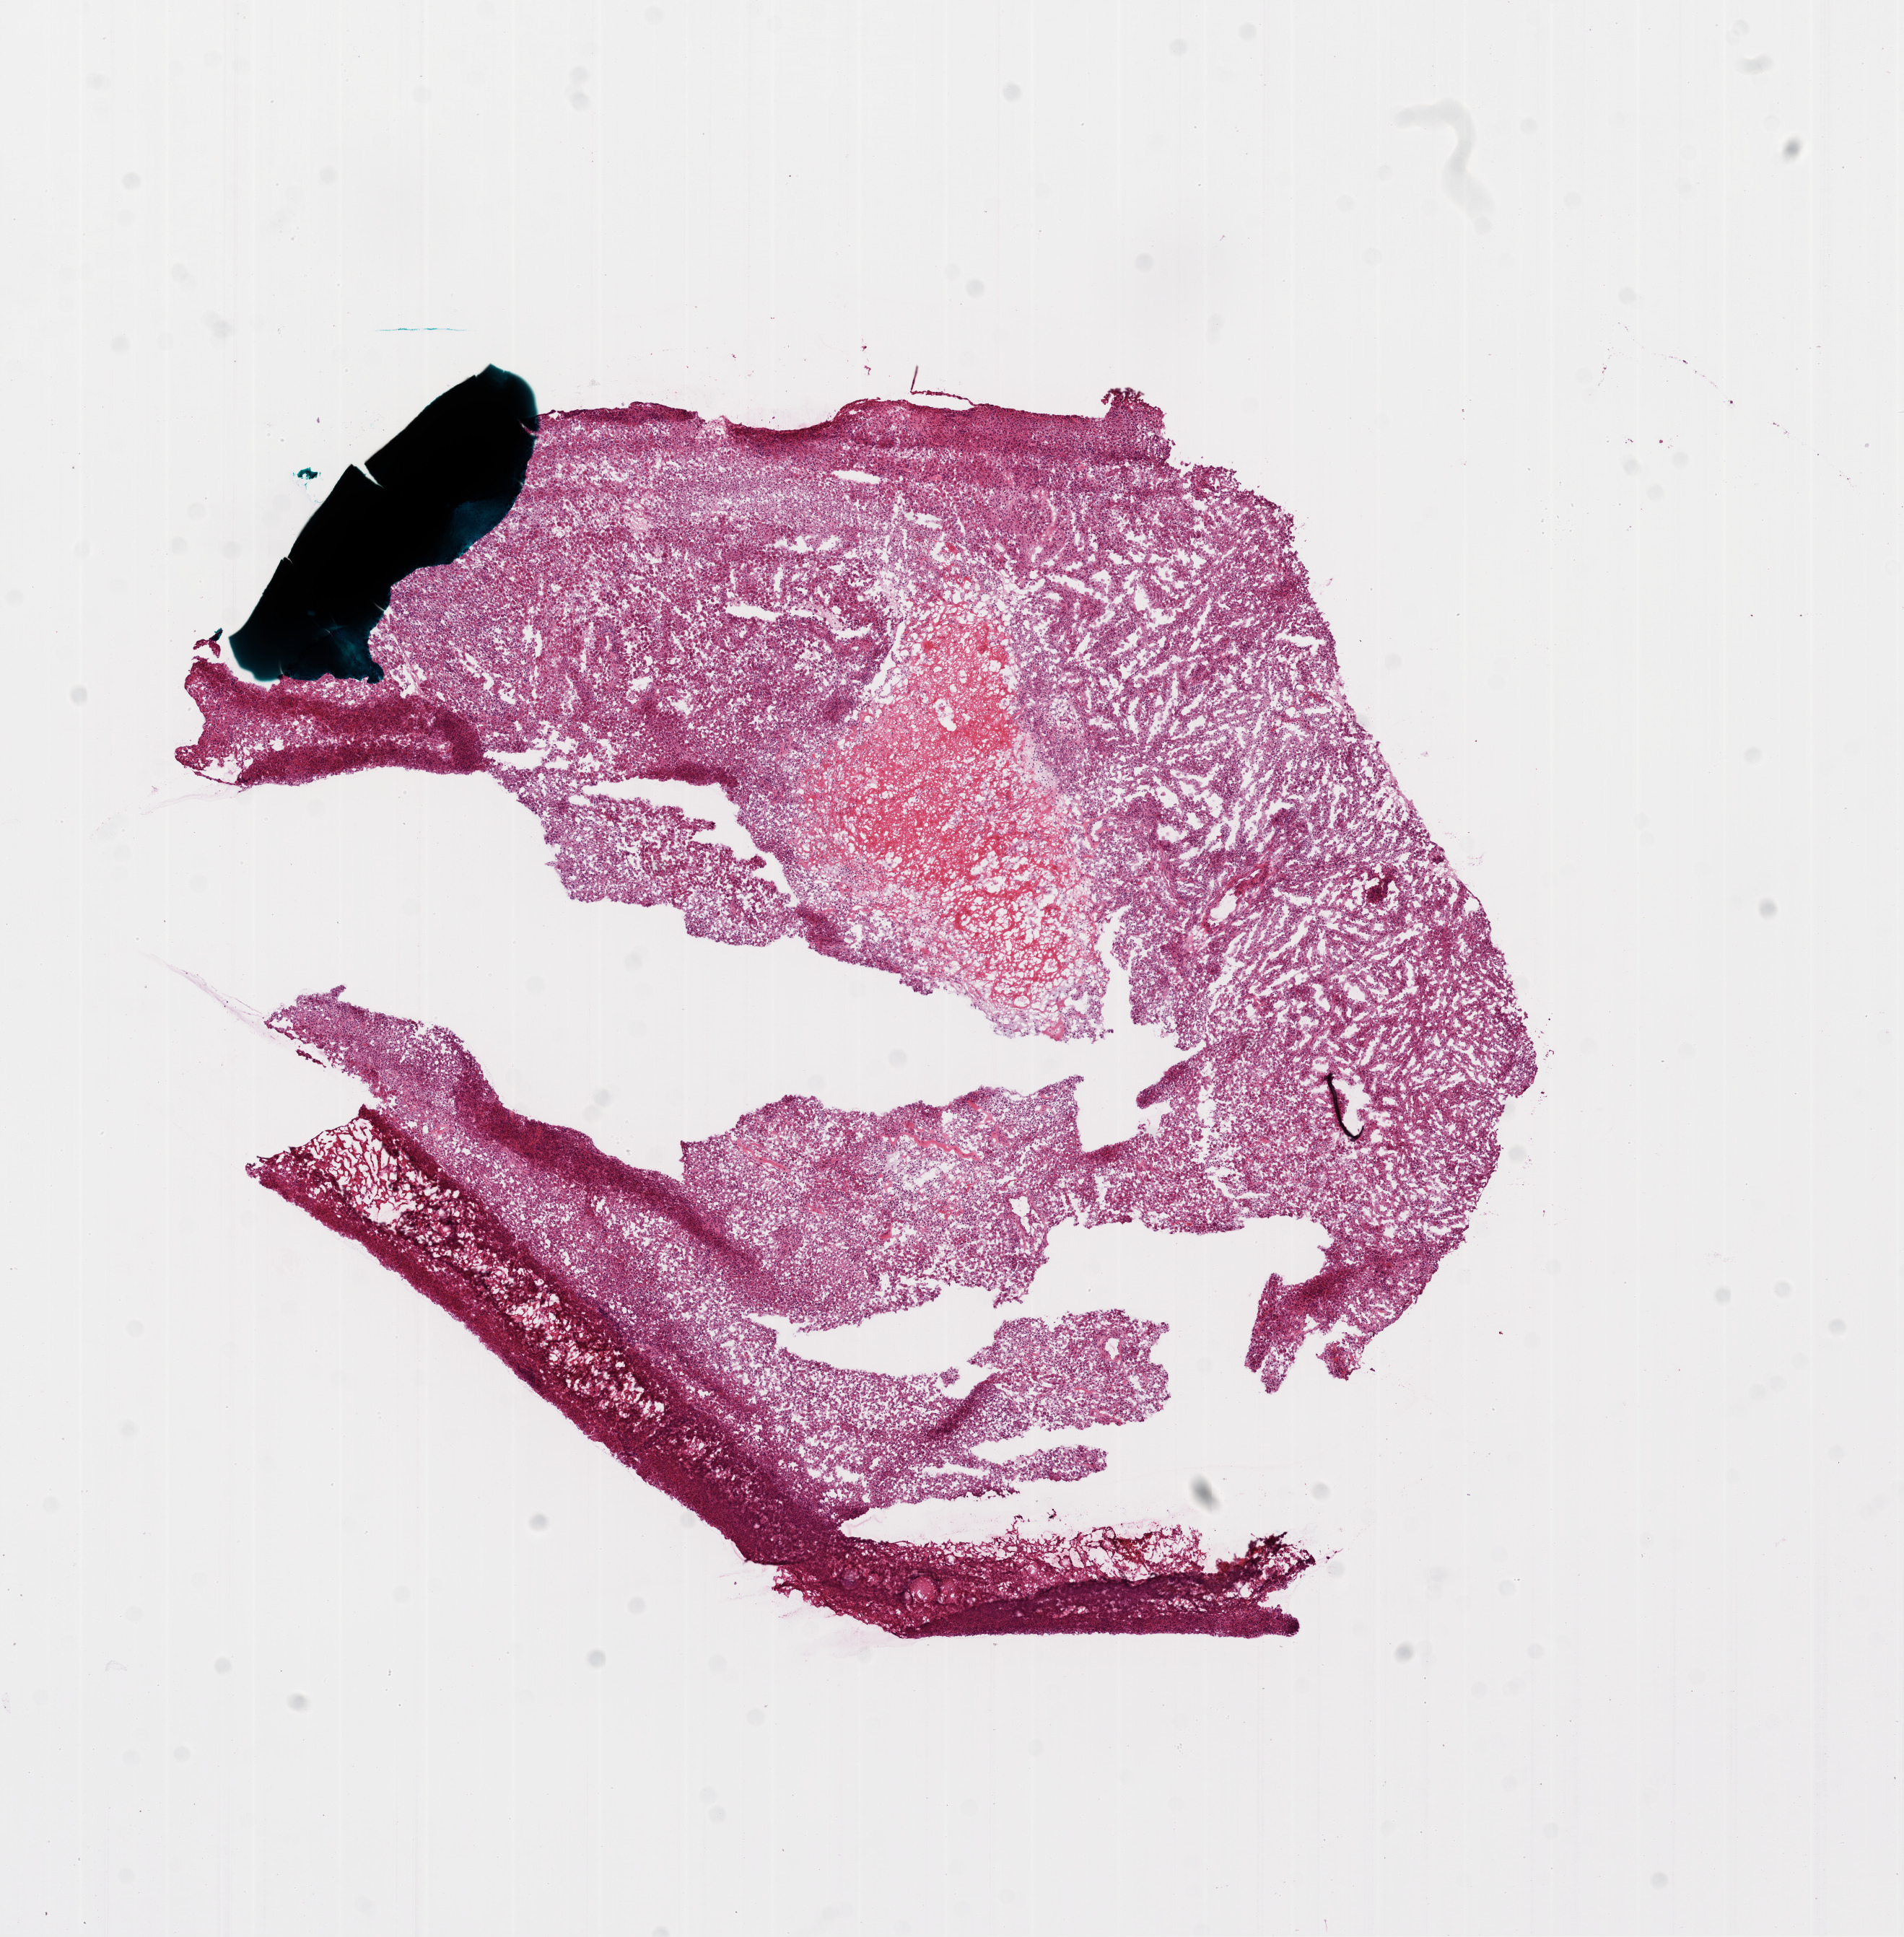
Whole-slide histology image, Hematoxylin and eosin (H&E) stained, low-resolution overview of the scanned area, about 10.6 x 10.8 mm (acquisition: 20x scan); frozen section from the bottom of the tissue portion; primary tumour sample from the brain. Male, age 49 years at initial diagnosis. Pathologist review of this section (percent, as recorded): tumour cells 80%, tumour nuclei 90%, necrosis 20%. Infiltration values recorded for this section: monocyte infiltration 100%.
Diagnosis: Glioblastoma.